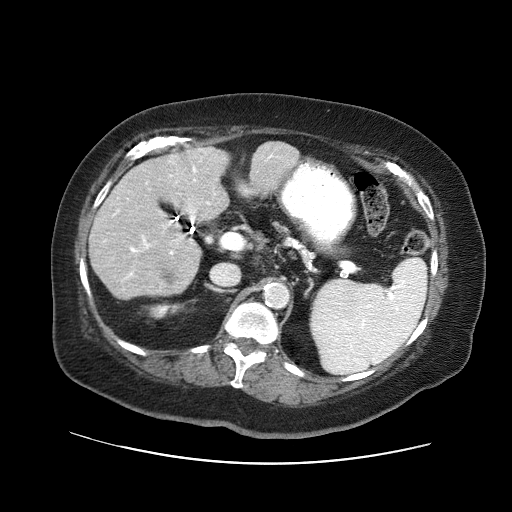
Contrast-enhanced abdominal CT (liver protocol), one axial slice. Position 24 of 71 along the scan axis. Reconstruction kernel STANDARD. Soft-tissue window (W 400 / L 40 HU). 2.5 mm slice thickness. 512 × 512 image matrix, field of view 400 × 400 mm. From the clinical record (not read from this slice): diagnosis: hepatocellular carcinoma (patient treated with transarterial chemoembolisation; whether this scan precedes or follows treatment is not stated here); TNM stage (as recorded): Stage-II; Child-Pugh class: A; tumour nodularity: multinodular.
Structures marked on this image (semi-automatically segmented with operator editing):
- liver parenchyma outside the tumour (the mass and vessels are separate outlines, so this box may not span the whole liver): bounding box (x1, y1, x2, y2) in pixels: (90, 144, 272, 298)
- mass: (158, 267, 177, 285)
- liver vessels: (104, 149, 215, 280)